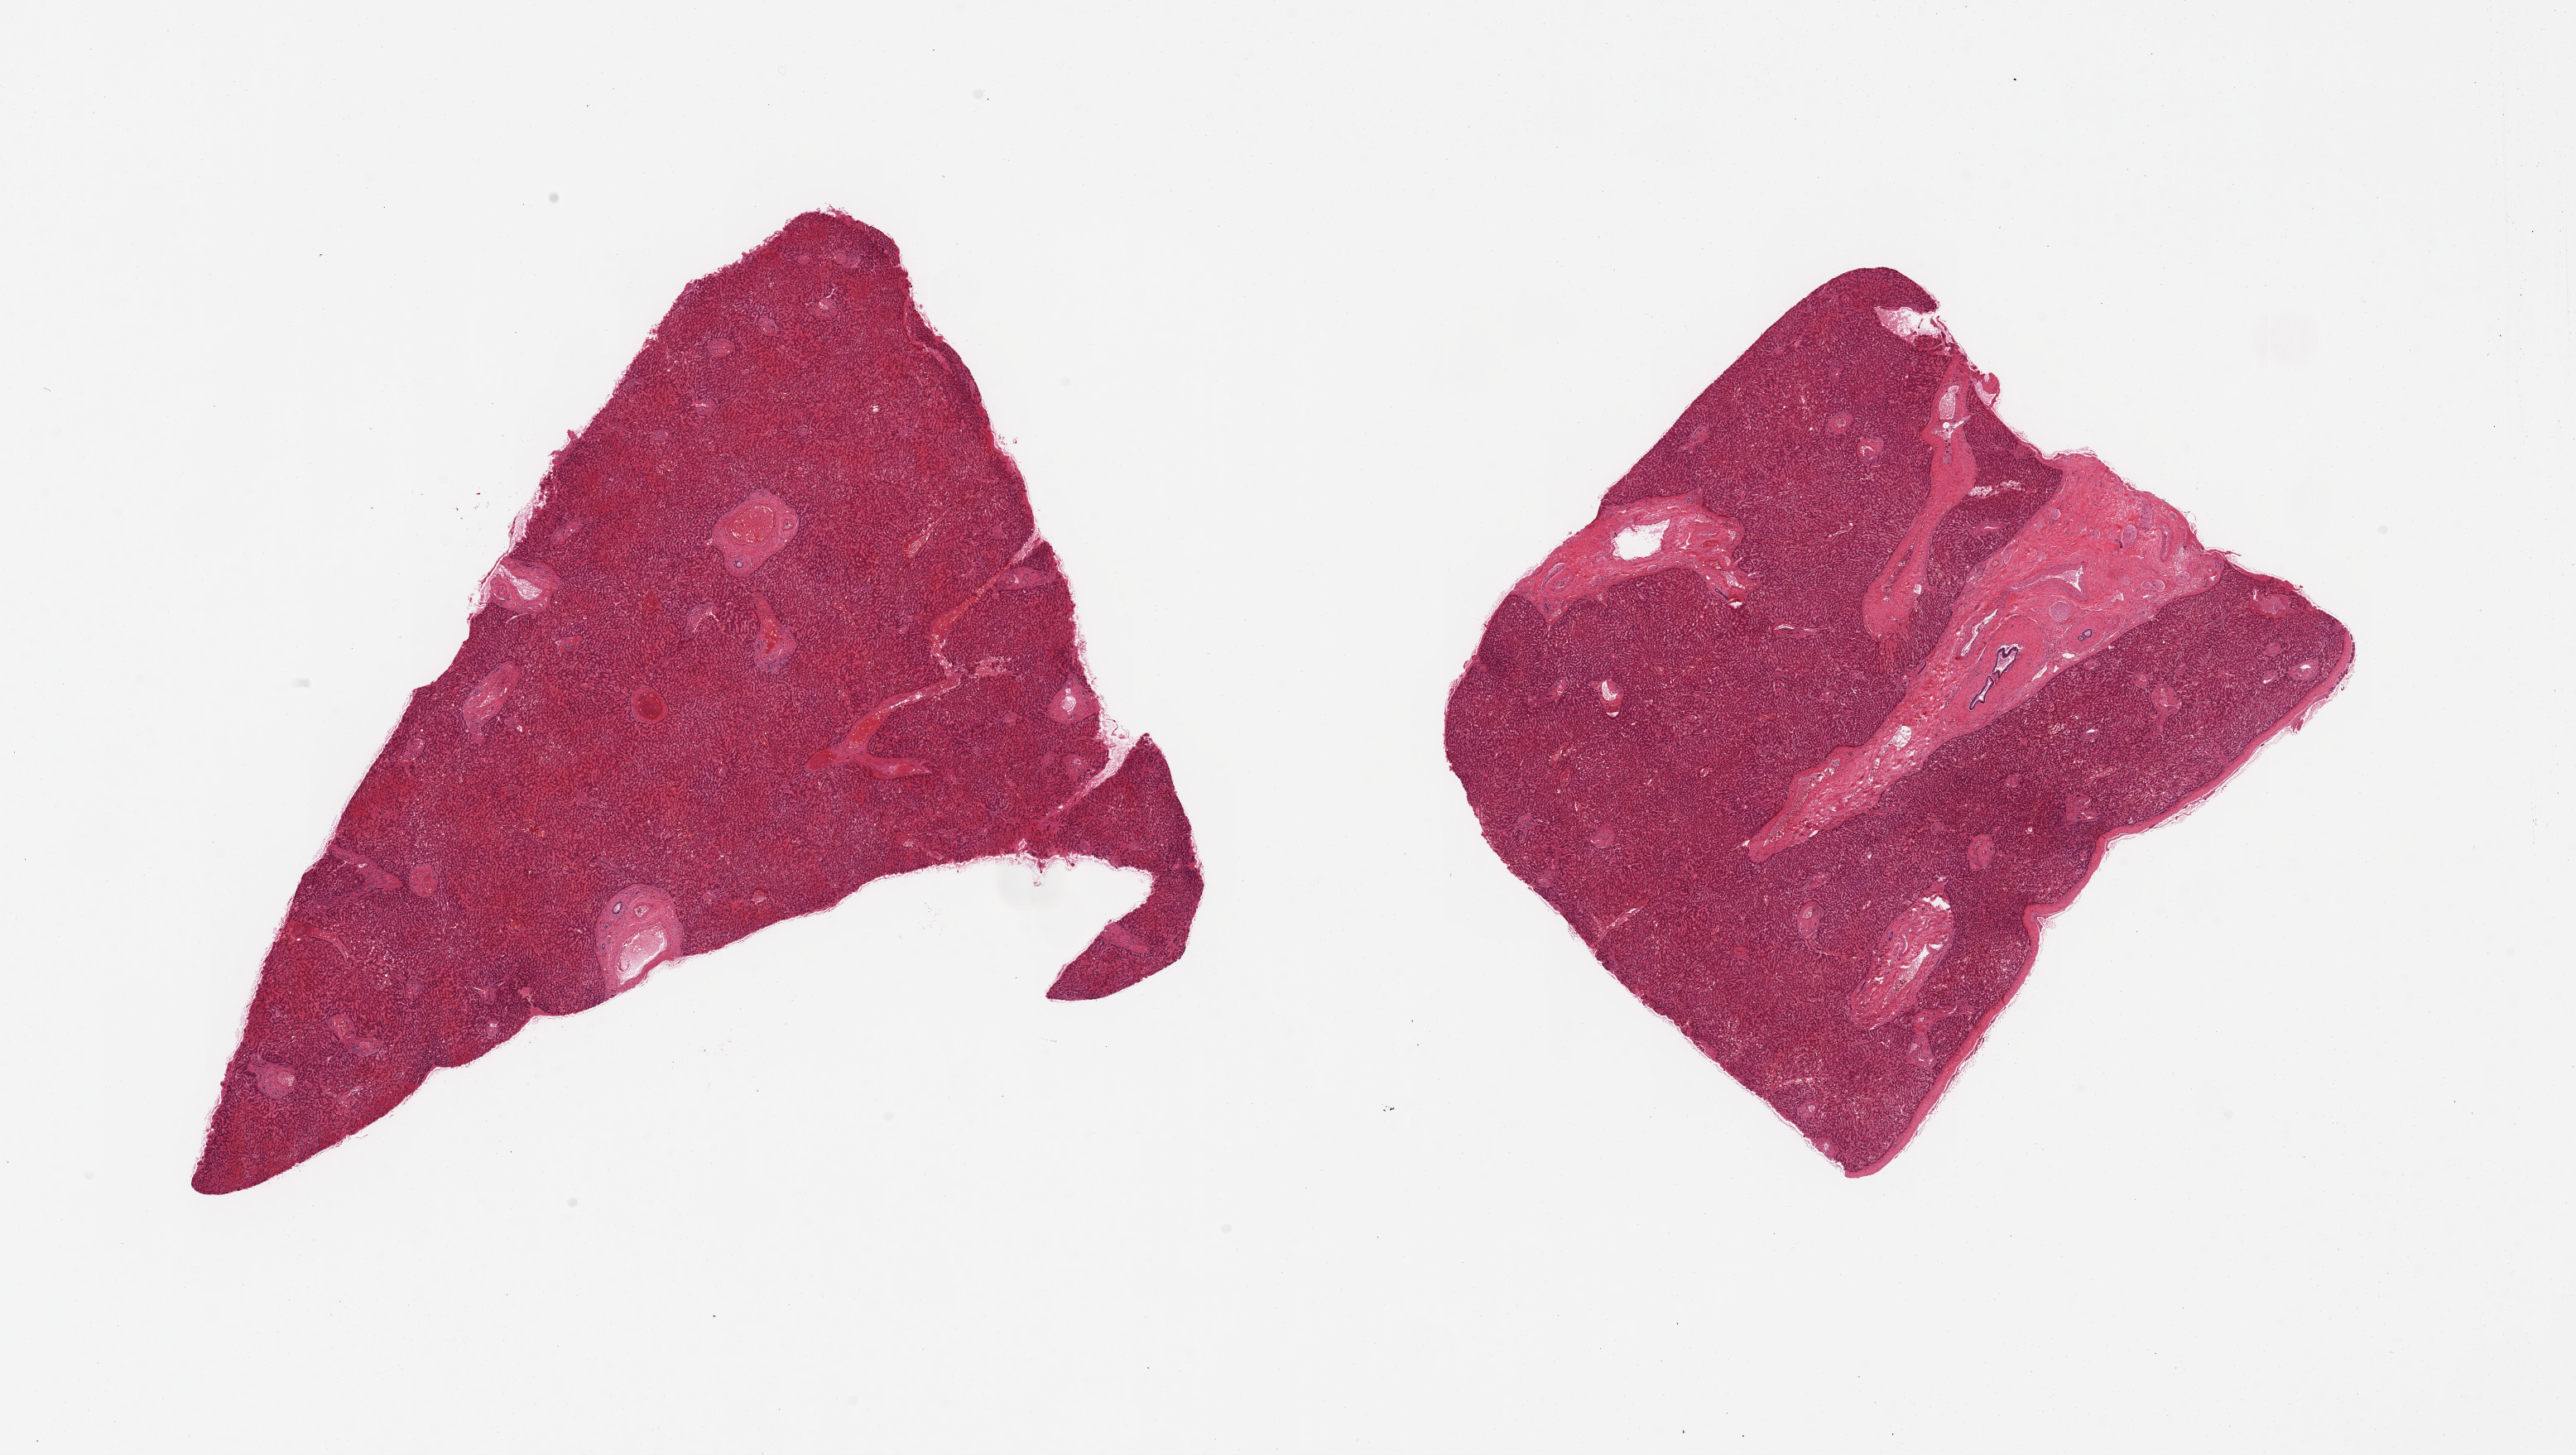
Digitized H&E-stained section — low-resolution overview of the scanned area, about 24.6 x 13.9 mm (acquisition: 20x scan), PAXgene-fixed, paraffin-embedded tissue, target tissue: liver, donor tissue sample. Donor sex: male.
Pathologist's review note for this sample: 2 pieces, 10-20% hilar fibrous connective elements.